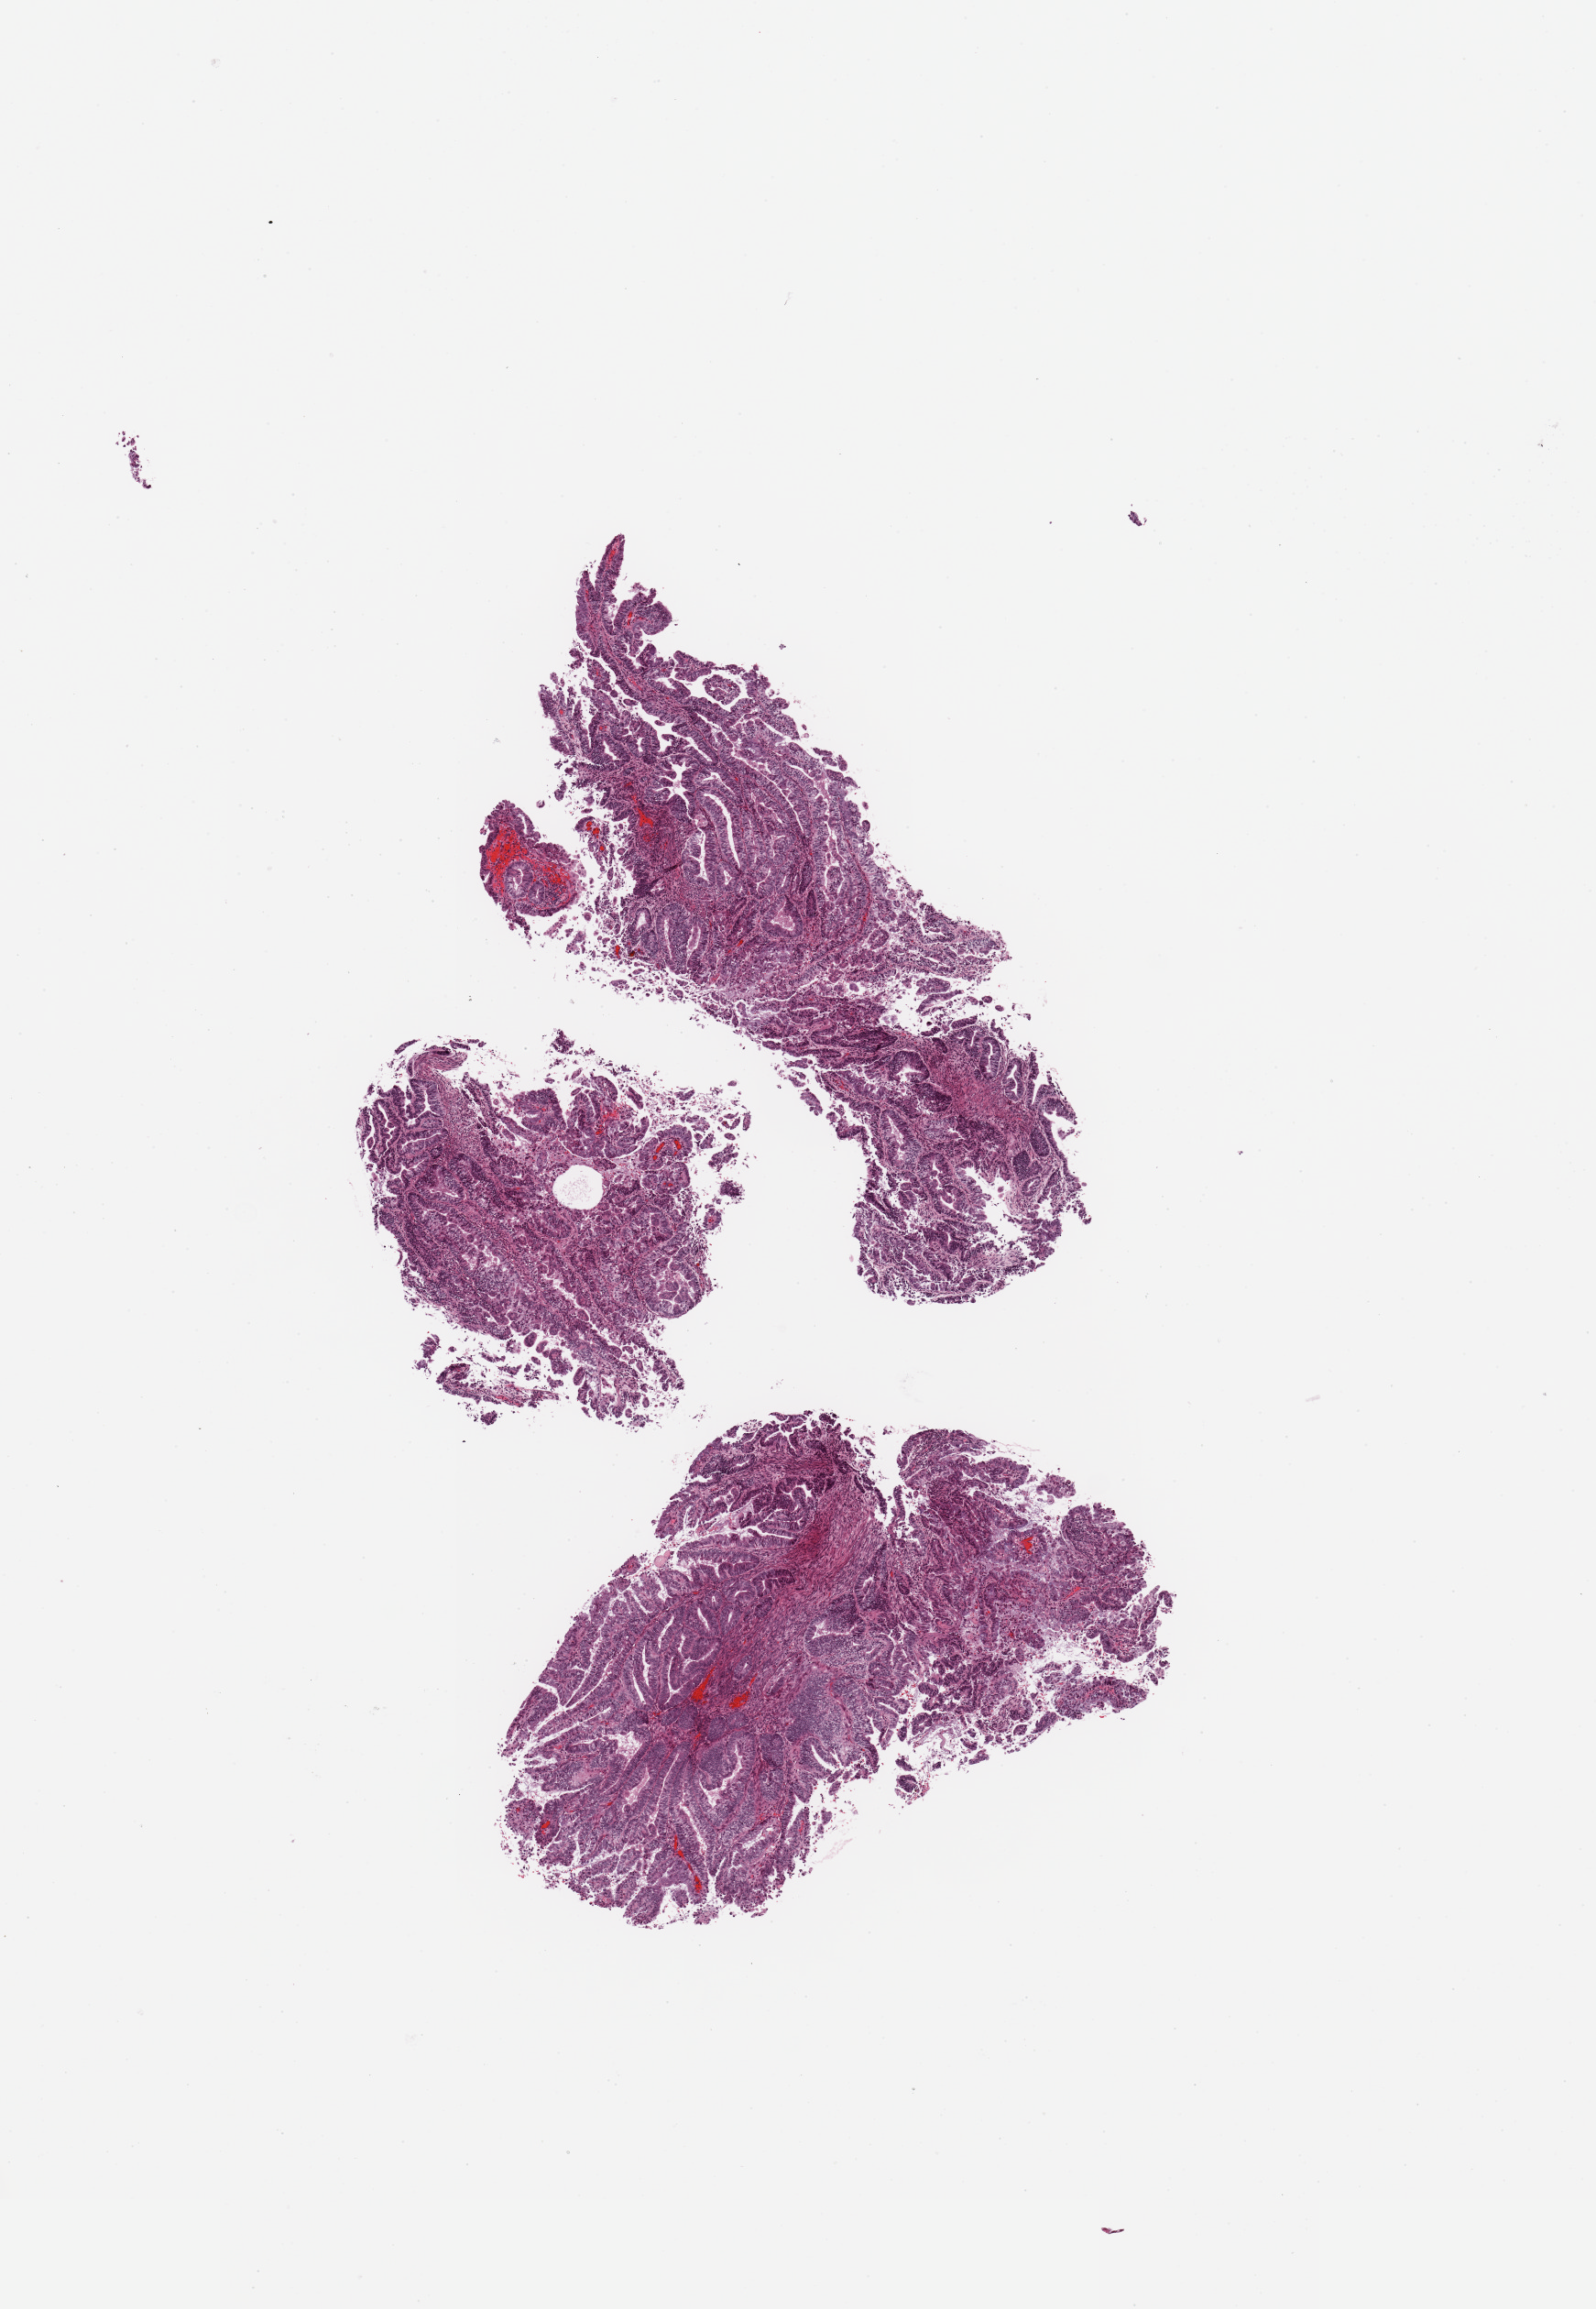
Whole-slide histology image, Hematoxylin and eosin (H&E) stained, a low-resolution overview of the entire scanned area, about 6.9 x 10.0 mm. Tumour tissue sample, sampled site: uterus. 65-year-old female patient. Histologic grade: G2 (moderately differentiated). Pathologist review of this section (percent, as recorded): tumour nuclei 90%, necrosis 1%.
Histologic diagnosis: Endometrioid adenocarcinoma, NOS. AJCC pathologic stage: I.